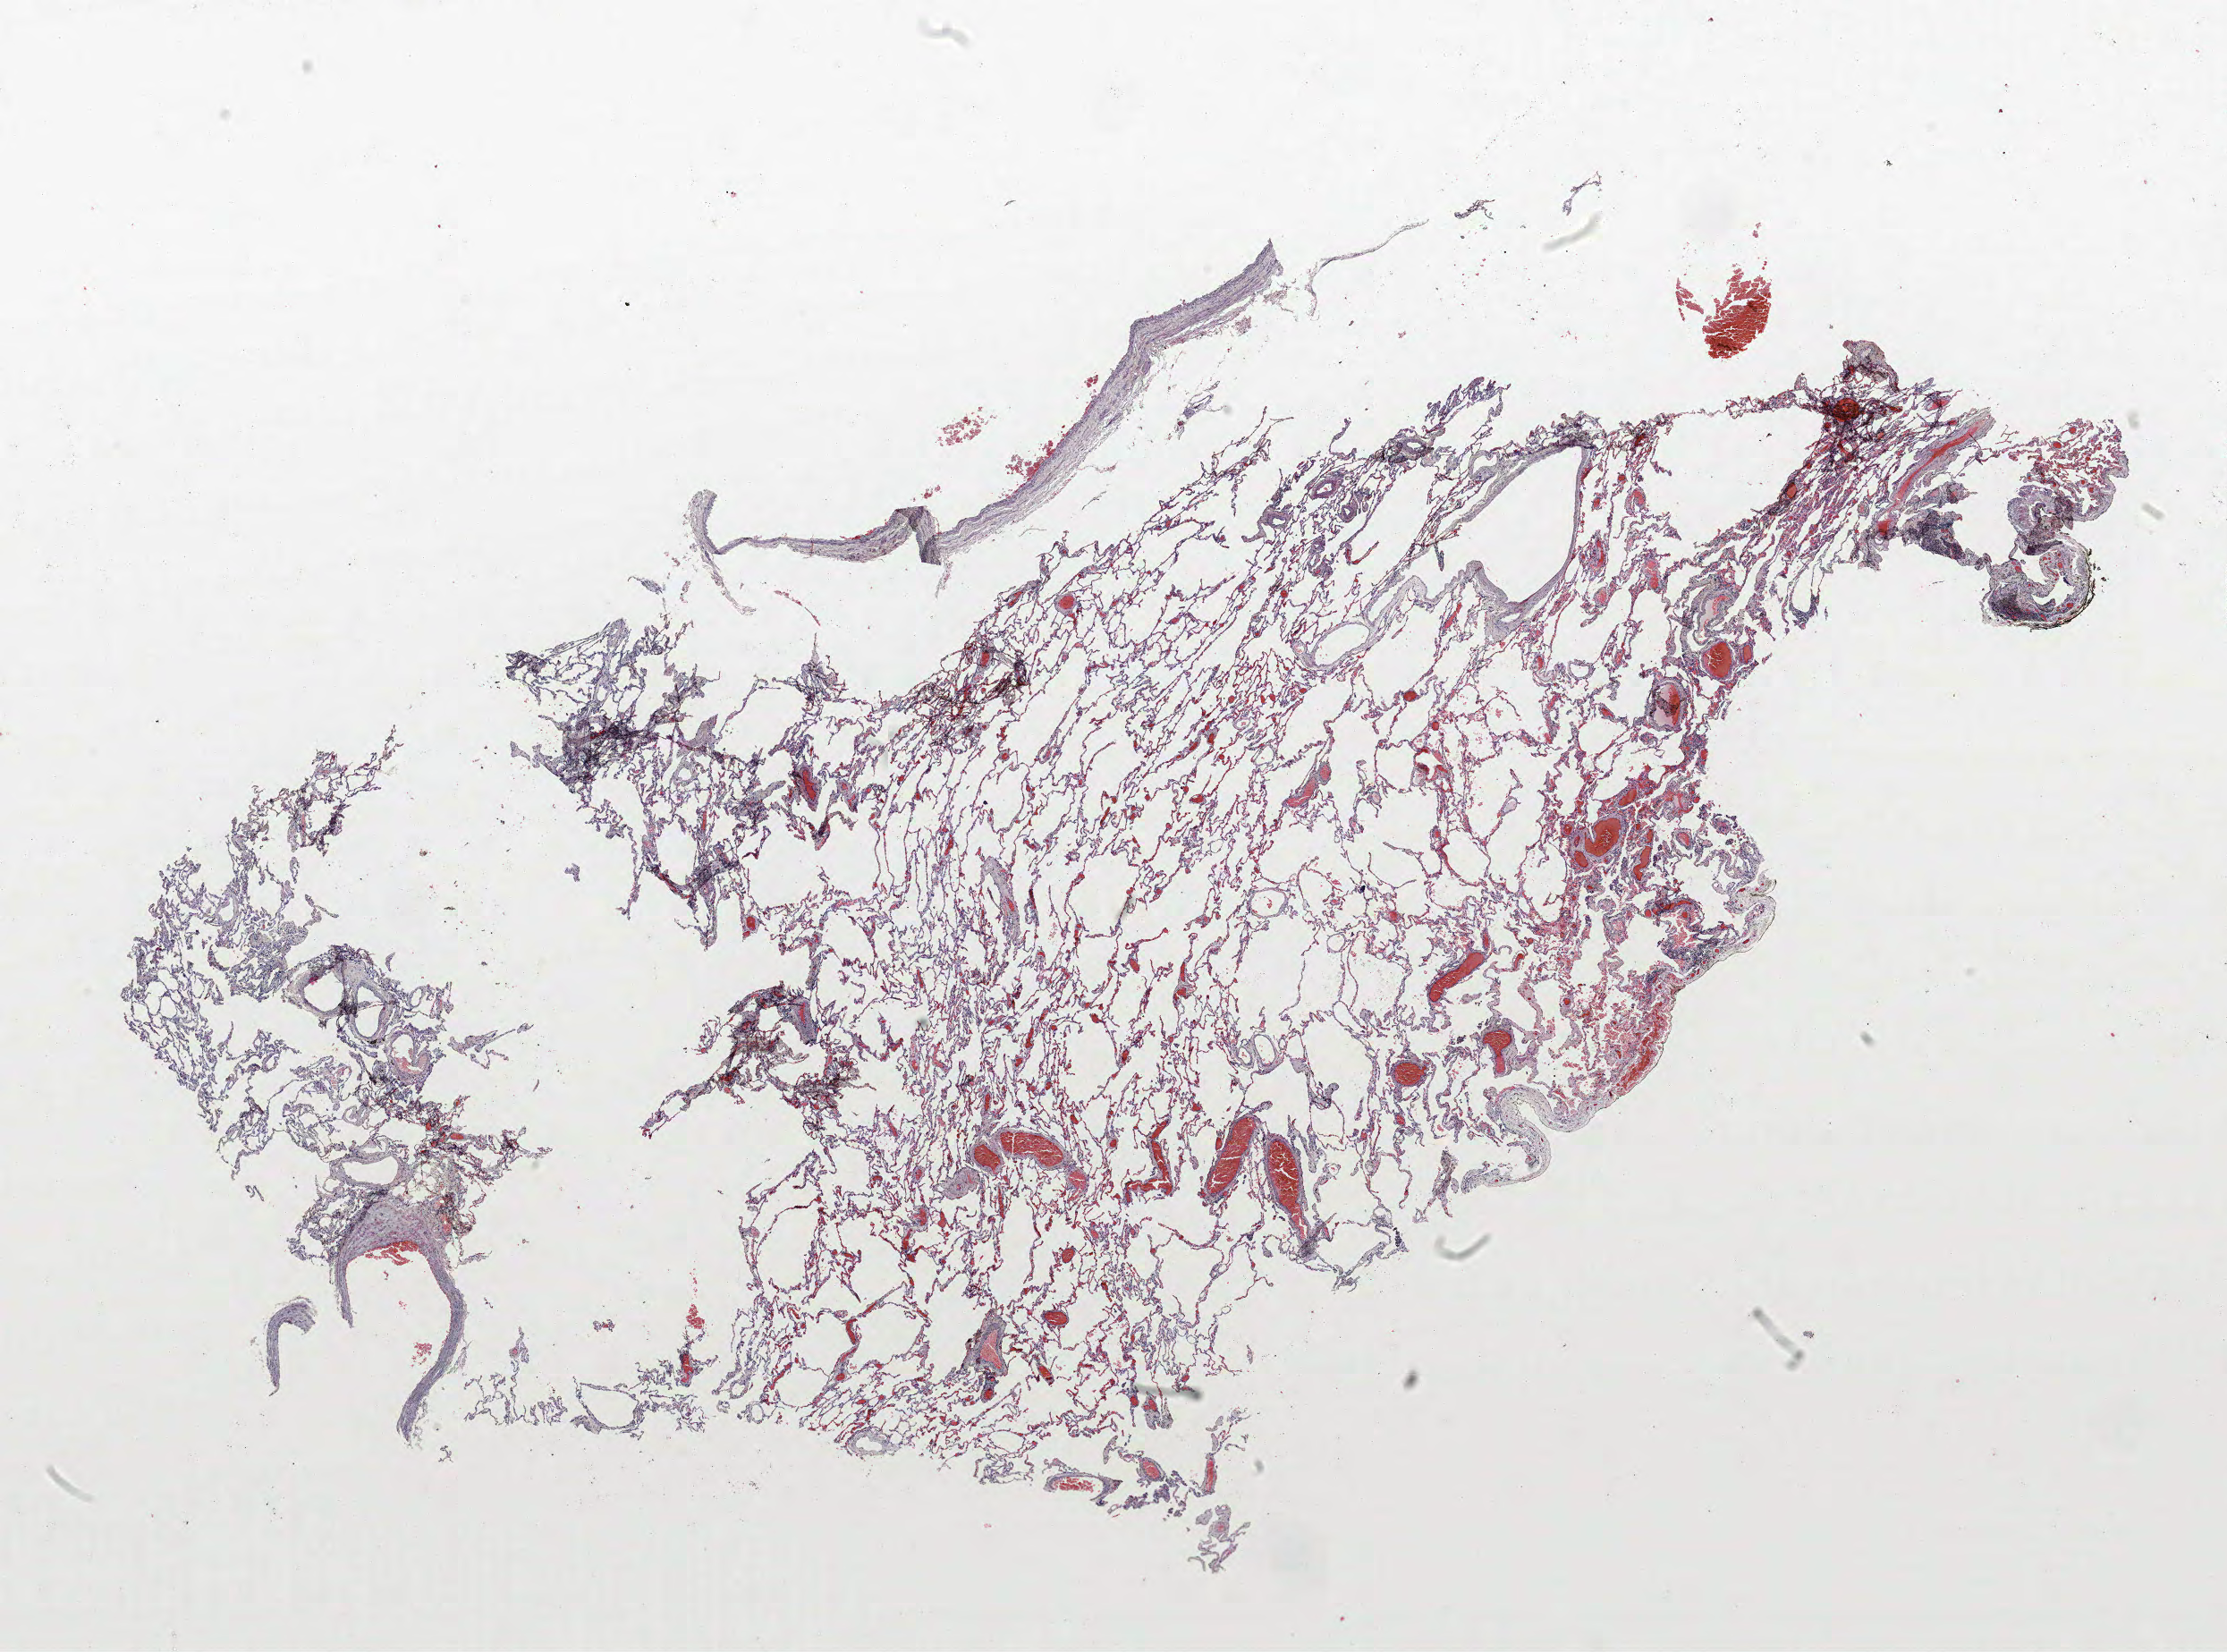
Whole-slide histology image, Hematoxylin and eosin (H&E) stained, whole scanned area (about 19.9 x 14.8 mm, slide scanned at 40x) shown as a low-resolution overview, formalin-fixed paraffin-embedded (FFPE) section, lung tissue. Male patient, aged 72 at enrolment. Current smoker at enrolment. Grade: moderately differentiated (G2).
Tumour size (pathology): 25 mm. Stage (AJCC 6th edition): IIA. Participant's lung-cancer diagnosis: Squamous cell carcinoma, NOS (ICD-O-3 8070/3). ICD-O-3 topography: upper lobe of lung (C34.1). Primary tumour location (clinical record): right upper lobe.